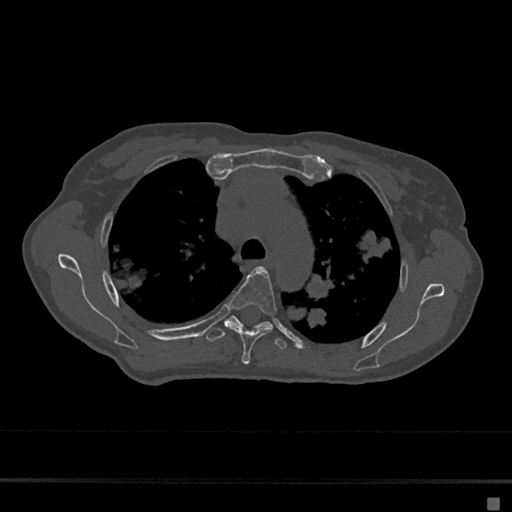
CT including the spine, one axial slice; slice 490 of 797 in the series (ordered by position); reconstruction kernel Br40s/3; 120 kVp; bone window (W 1800 / L 400 HU); 0.5 mm slice thickness; 512 × 512 image matrix, field of view 360 × 360 mm. Patient: female, 68 years. Case-level facts recorded for this patient, not image findings: primary cancer: renal.
Outlined on this slice (semi-automatically segmented with operator editing):
- T4 vertebra: box from (x=227, y=267) to (x=277, y=364) px
- T5 vertebra: (x=206, y=315)–(x=287, y=350)